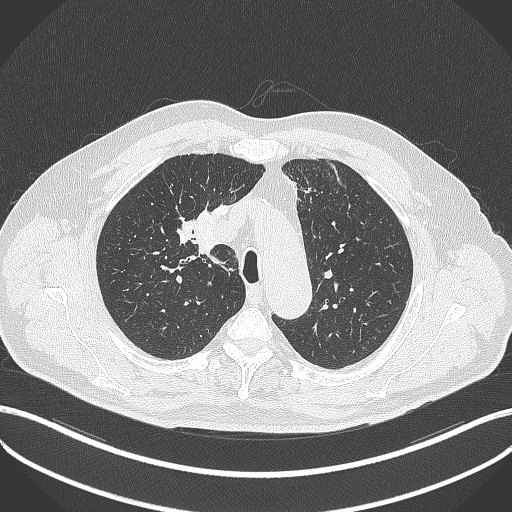
Chest CT, one axial slice. Position 294 of 411 along the scan axis. 120 kVp. Lung window (W 1500 / L -600 HU). 1 mm slice thickness. 512 × 512 image matrix, field of view 400 × 400 mm. Patient: male, 60 years. From the clinical record (not read from this slice): clinical TNM (as recorded): T1b N1 M0.
Outlined on this slice (rectangle marked by the reading radiologist):
- lung tumour (recorded histology: squamous cell carcinoma): bounding box (x1, y1, x2, y2) in pixels: (192, 209, 218, 259)